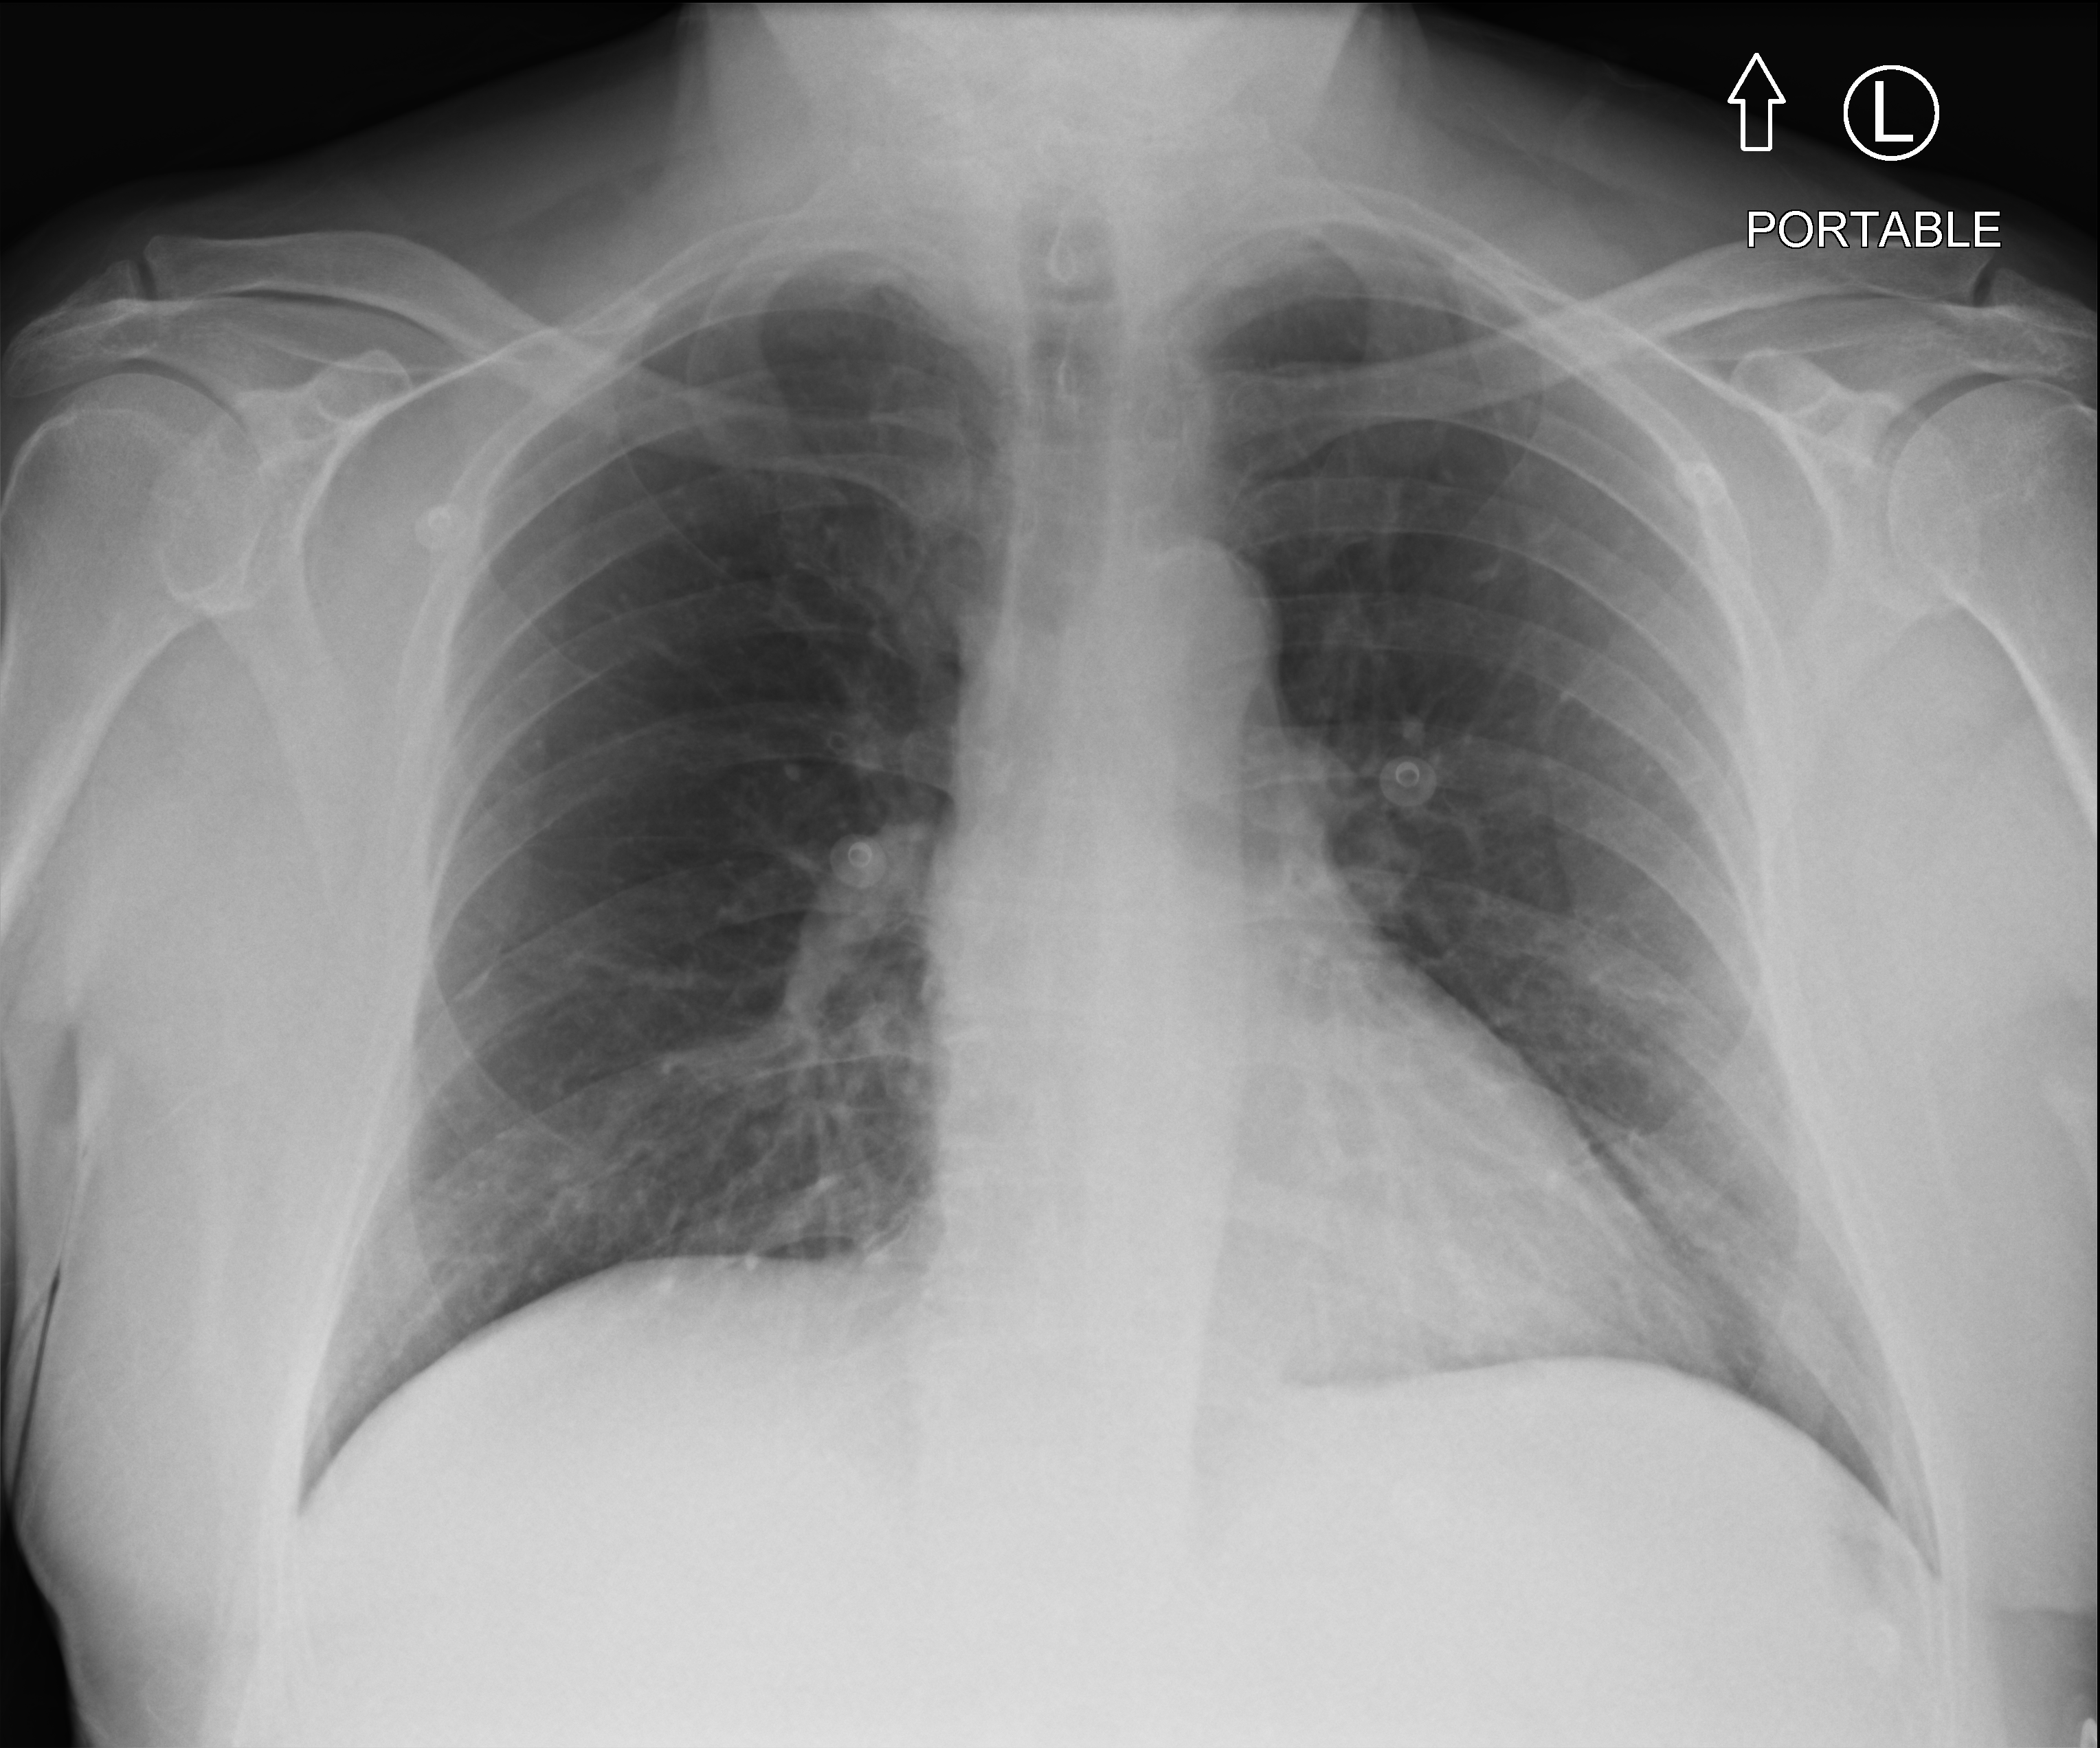
Bedside chest radiograph (computed radiography); anteroposterior (AP) projection. Male patient hospitalised with COVID-19, age 60–74 years.
Admission-level facts for this patient (not findings on this image; timing relative to this image not recorded): admitted to intensive care during this hospital stay: no; mechanically ventilated during this hospital stay: no.